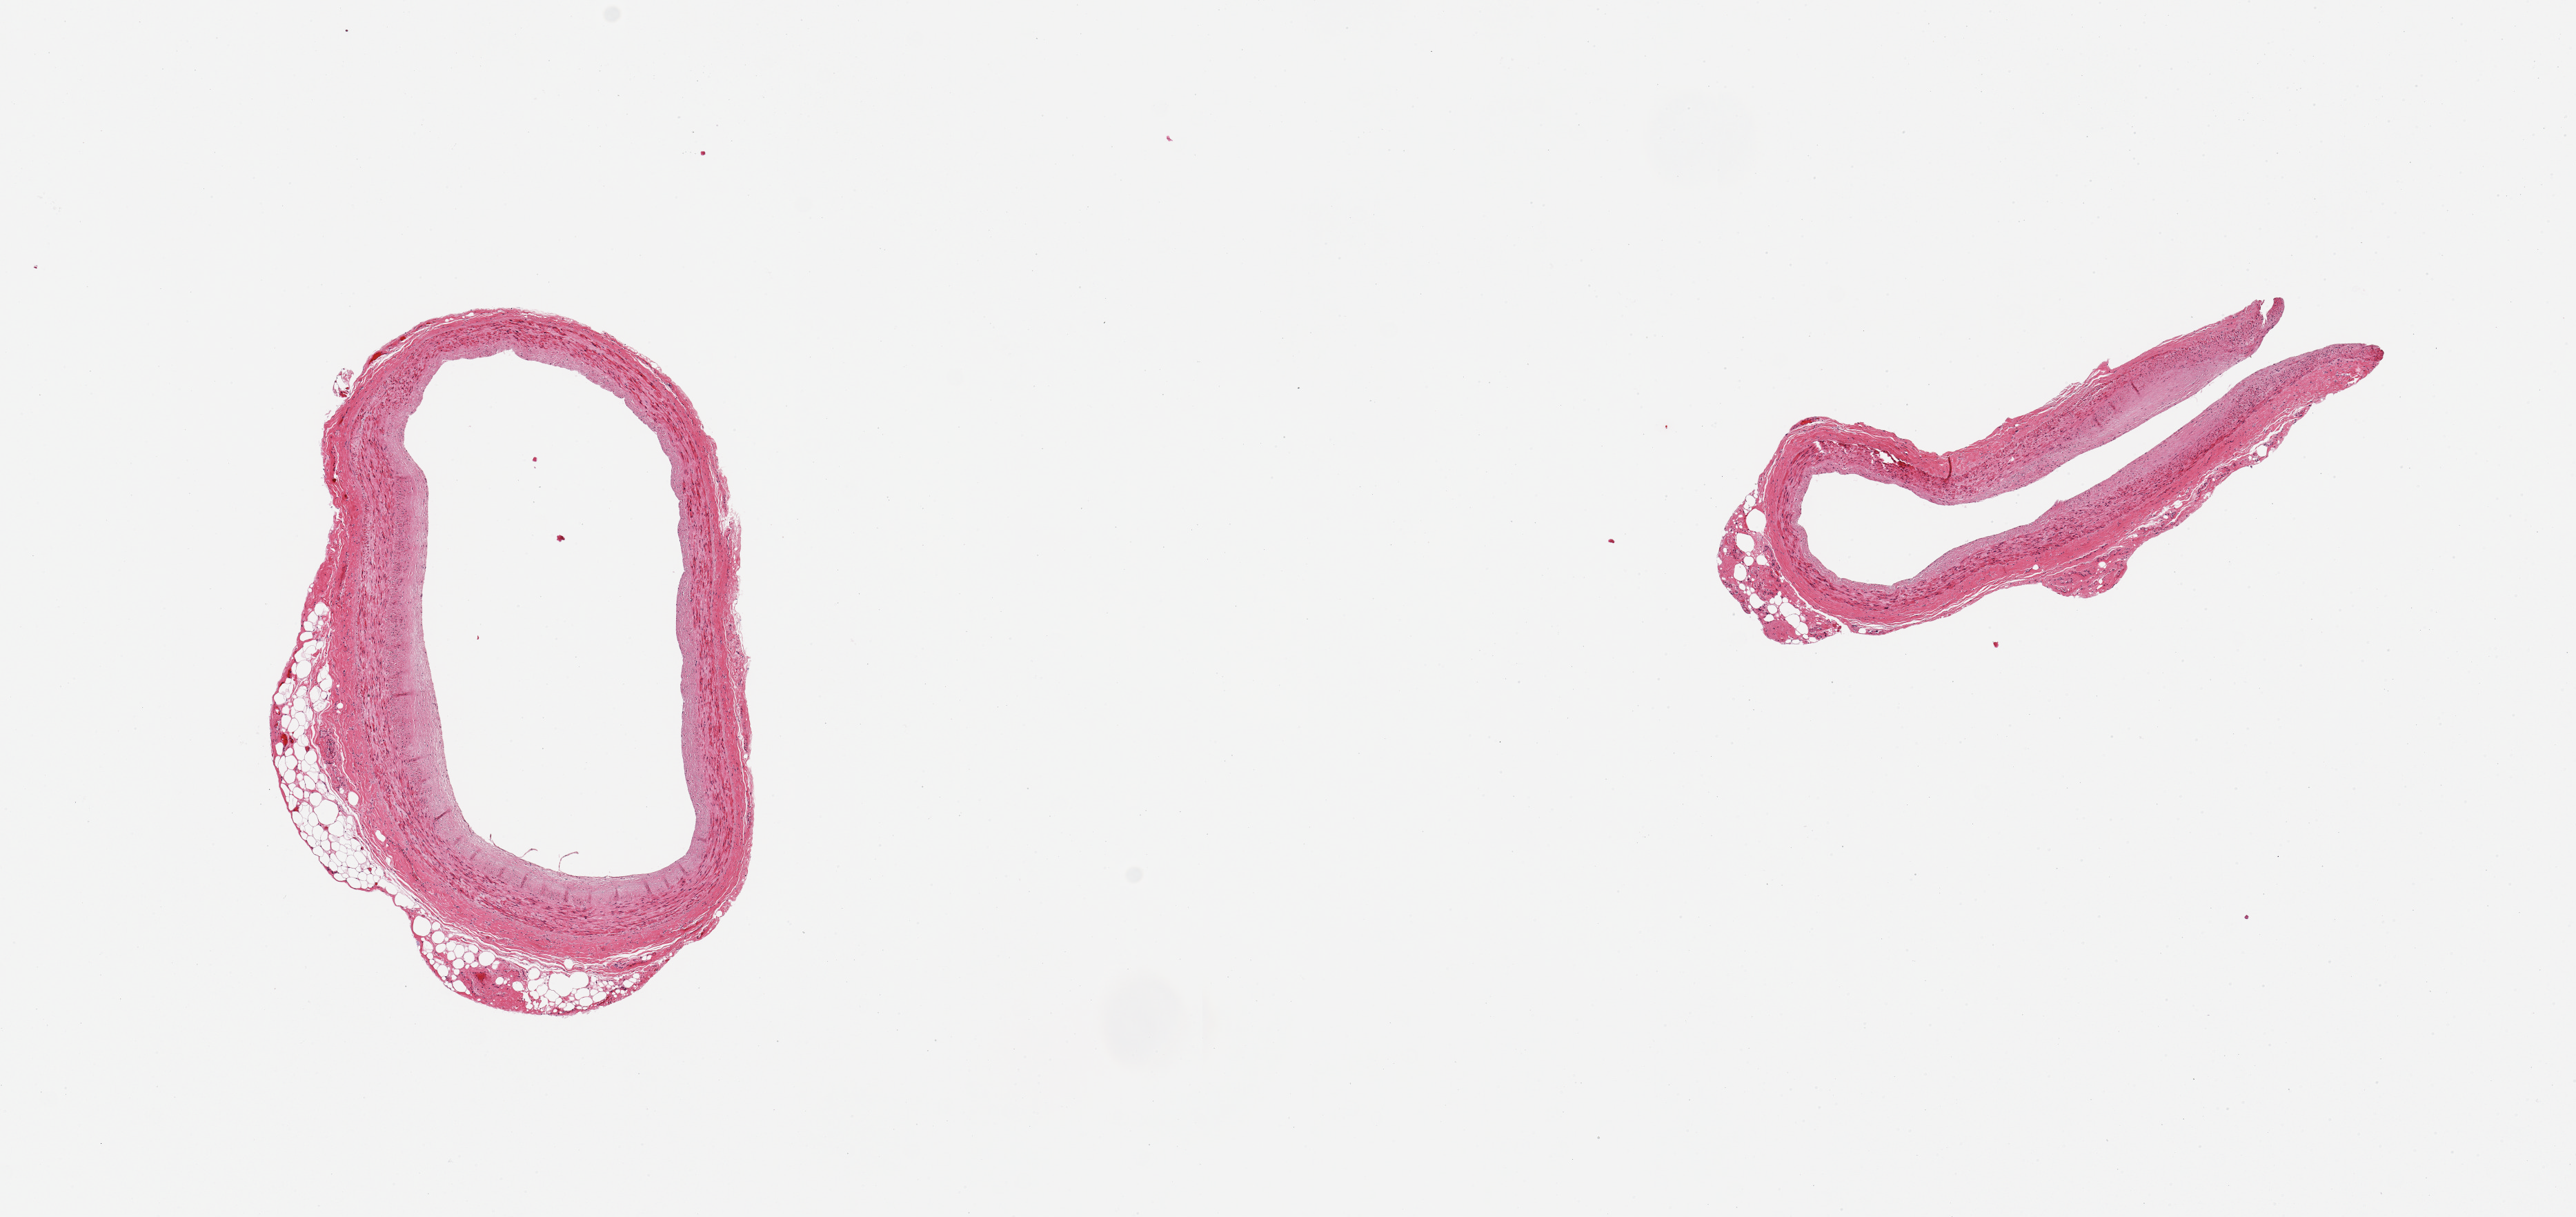
Digitized H&E-stained section, a low-resolution overview of the entire scanned area, about 14.8 x 7.0 mm; PAXgene-fixed paraffin-embedded (PFPE) section; target tissue: coronary artery; tissue donor sample. Female donor.
Pathologist's review note for this sample: 2 pieces; adherent fat up to 0.4mm, mild atherosclerosis.